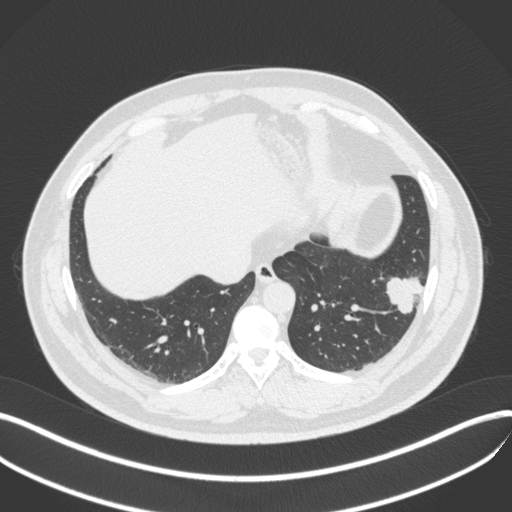
Chest CT, one axial slice. Slice 120 of 420 in the series (ordered by position). Reconstruction kernel B31f. Lung window (W 1500 / L -600 HU). 1 mm slice thickness. 512 × 512 image matrix, field of view 400 × 400 mm. Patient: male, 39 years. Case-level facts recorded for this patient, not image findings: clinical TNM (as recorded): T2a N0 M0.
Outlined on this slice (bounding box drawn by a radiologist):
- lung tumour (recorded histology: adenocarcinoma): bounding box (x1, y1, x2, y2) in pixels: (384, 269, 426, 318)